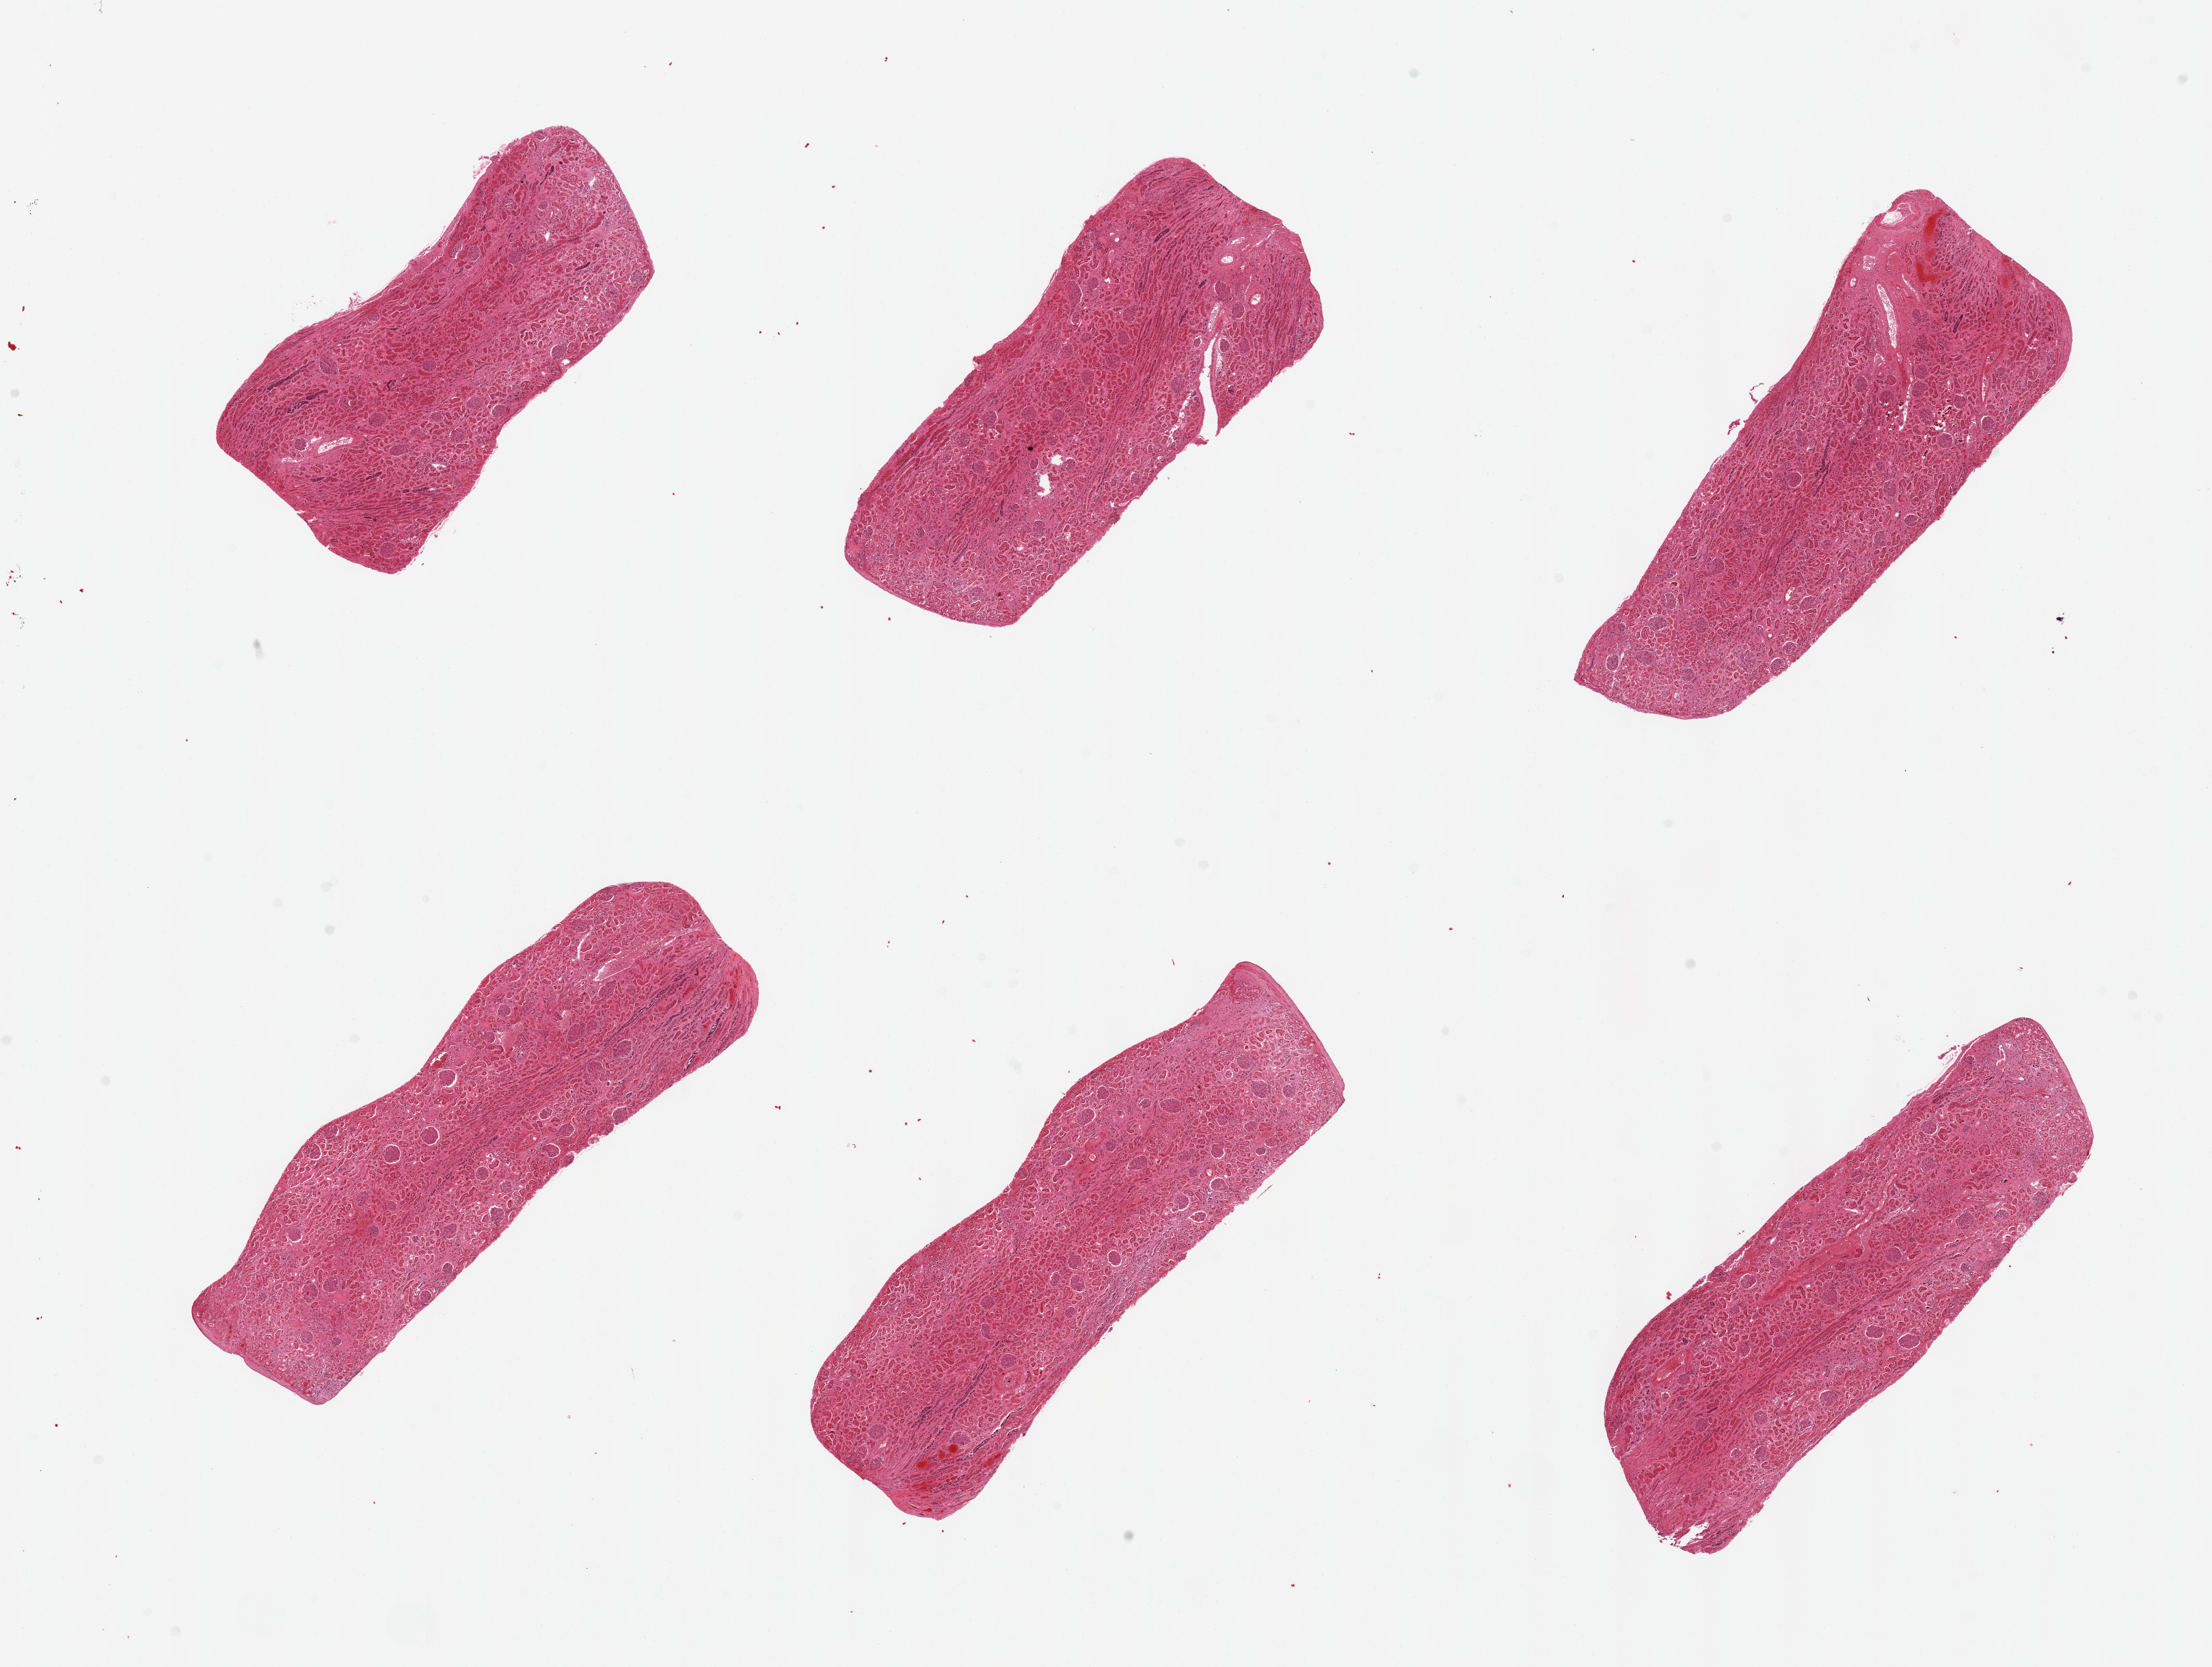
Digitized hematoxylin and eosin (H&E)-stained section — whole scanned area (about 25.6 x 19.3 mm, slide scanned at 20x) shown as a low-resolution overview, PAXgene-fixed paraffin-embedded (PFPE) section, section of renal cortex (target tissue), tissue donor sample. Donor: male.
- reviewer comment on this tissue sample: 6 pieces, glomeruli present in all sections, but advanced autolysis